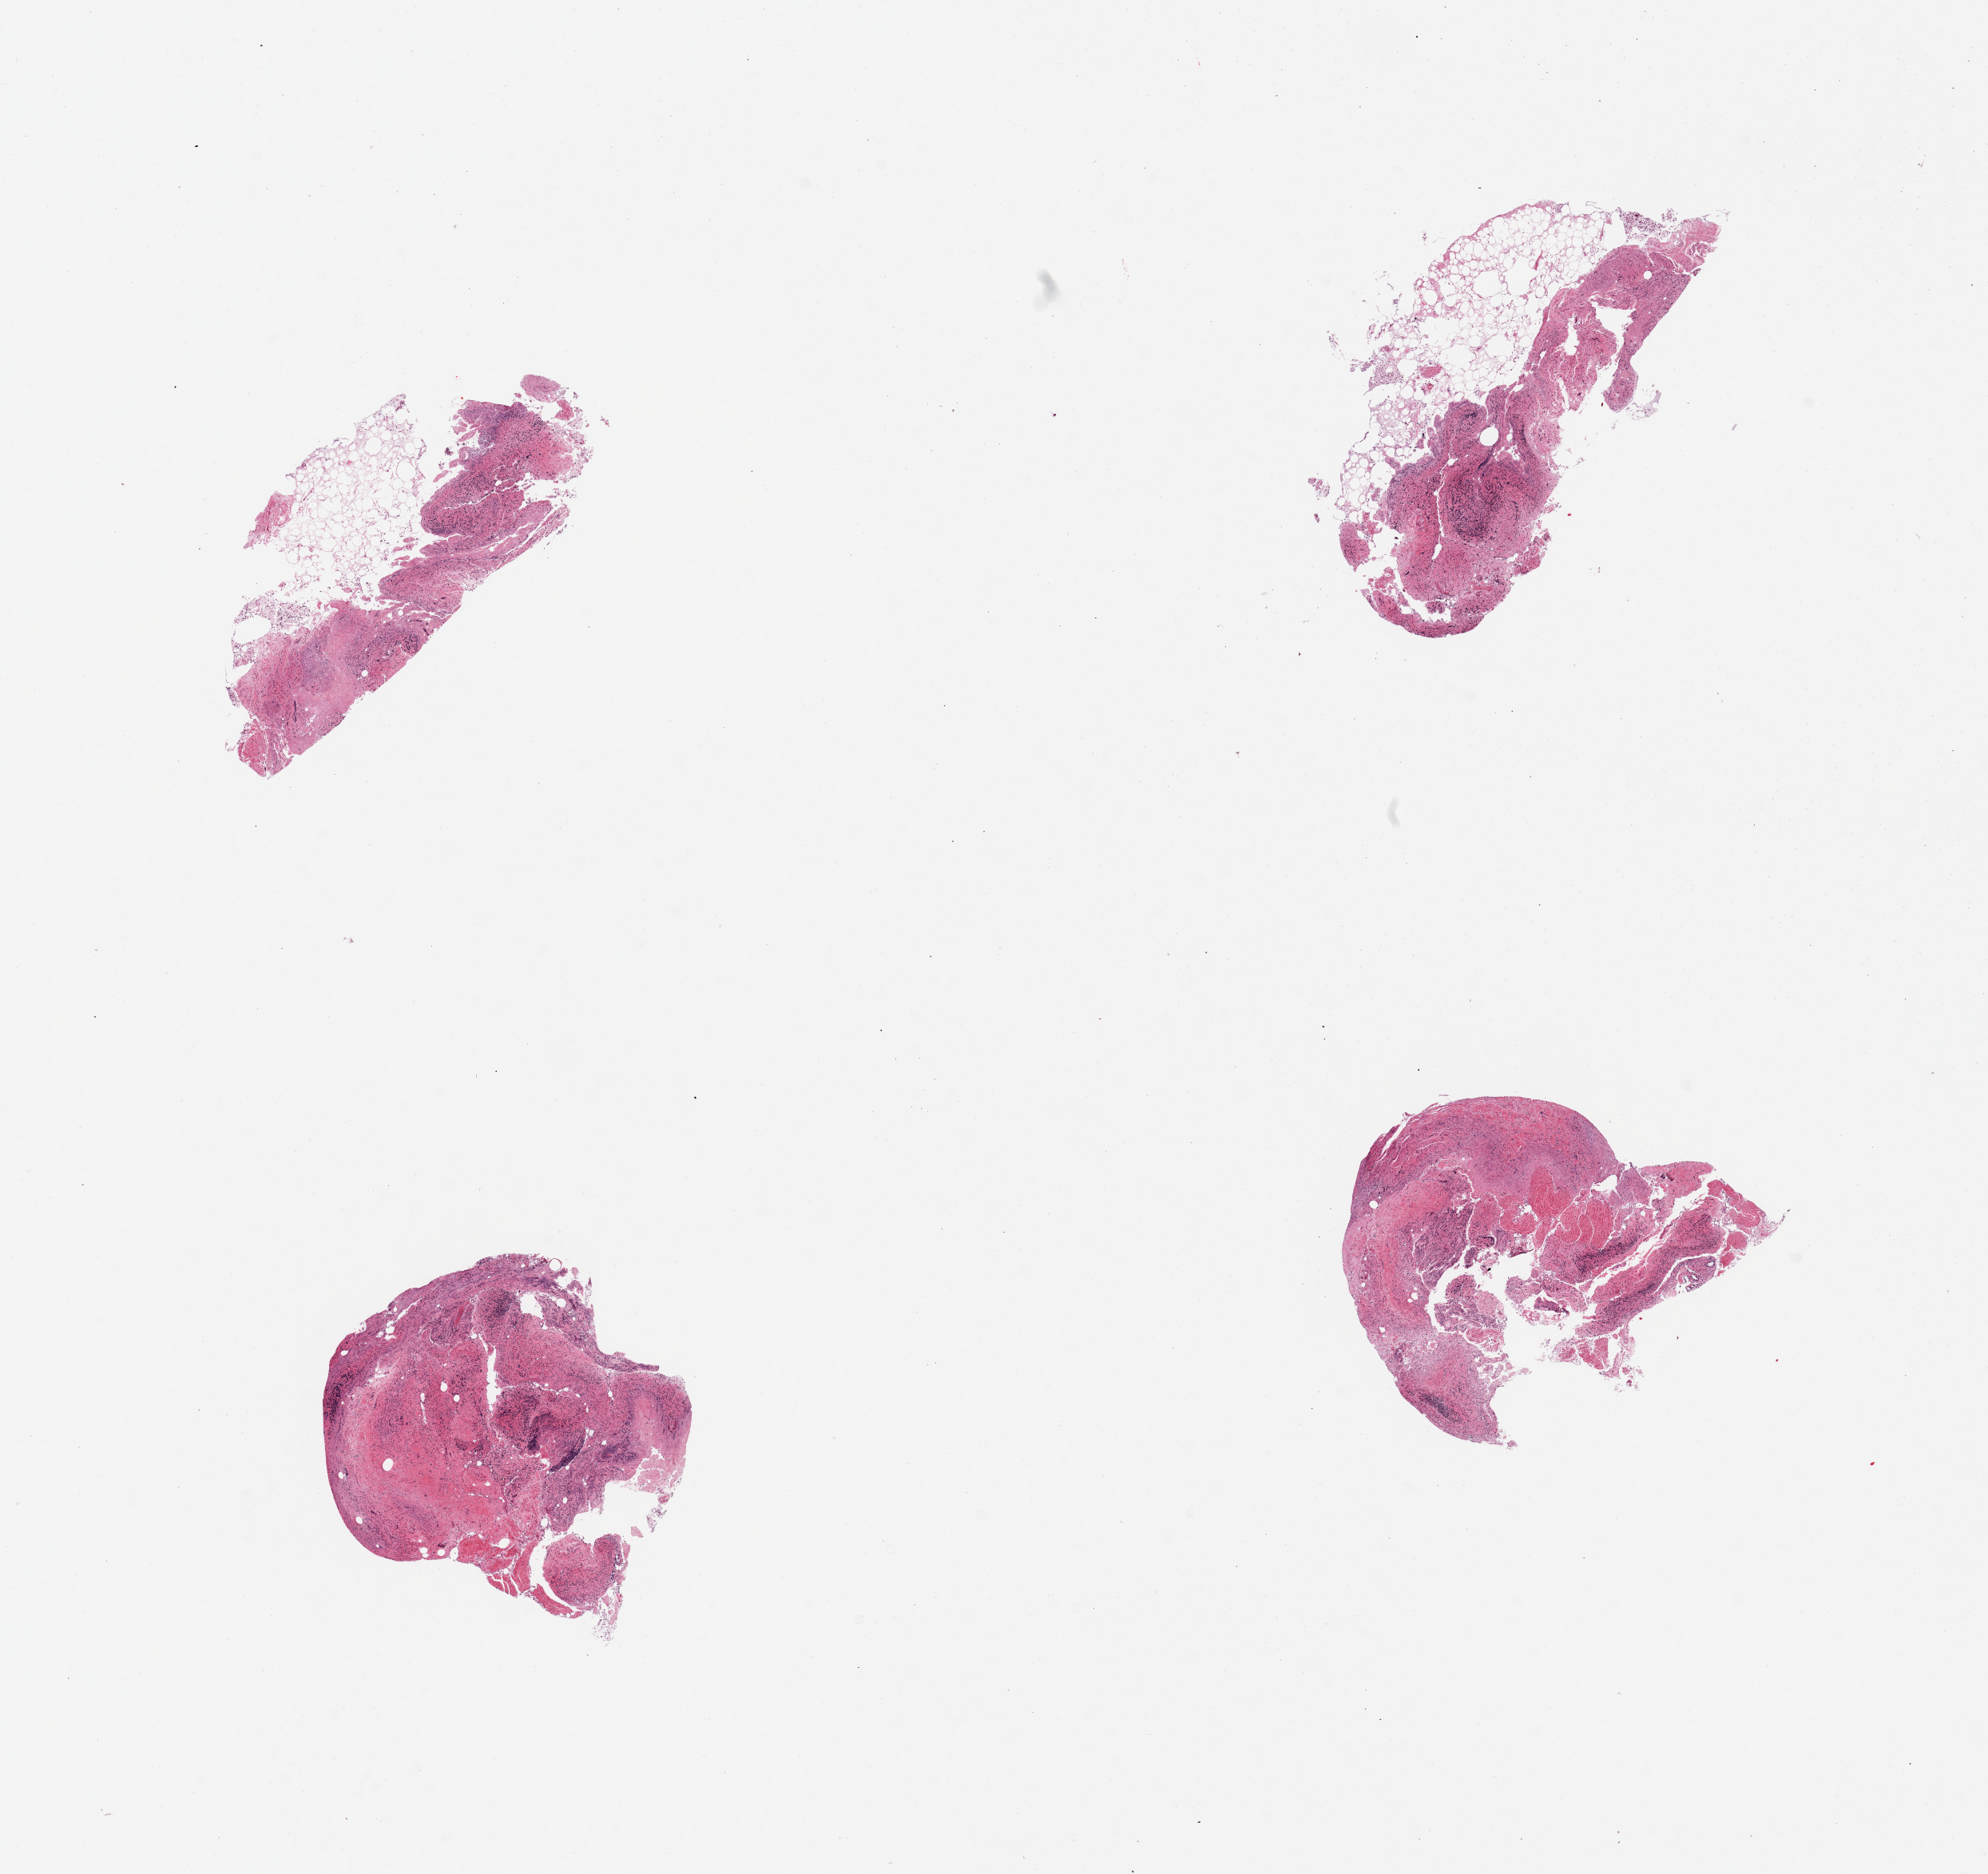
Digitized hematoxylin and eosin (H&E)-stained section, a low-resolution overview of the entire scanned area, about 19.7 x 18.6 mm; PAXgene-fixed paraffin-embedded (PFPE) section; section of ileum (target tissue); donor tissue sample. Female donor.
Reviewer comment on this tissue sample: 4 pieces, fragments of autolyzed mucosa and strips of fat and muscularis, limited lymphoid tissue.